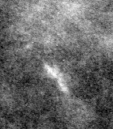
Region of interest cut from a scanned film mammogram (one marked finding), left breast, CC view, BI-RADS breast density category 2 (scale 1–4).
Marked abnormality: calcifications, morphology fine linear branching, distribution clustered / linear; BI-RADS assessment category 4; pathology result (as recorded, not read from the image): malignant.